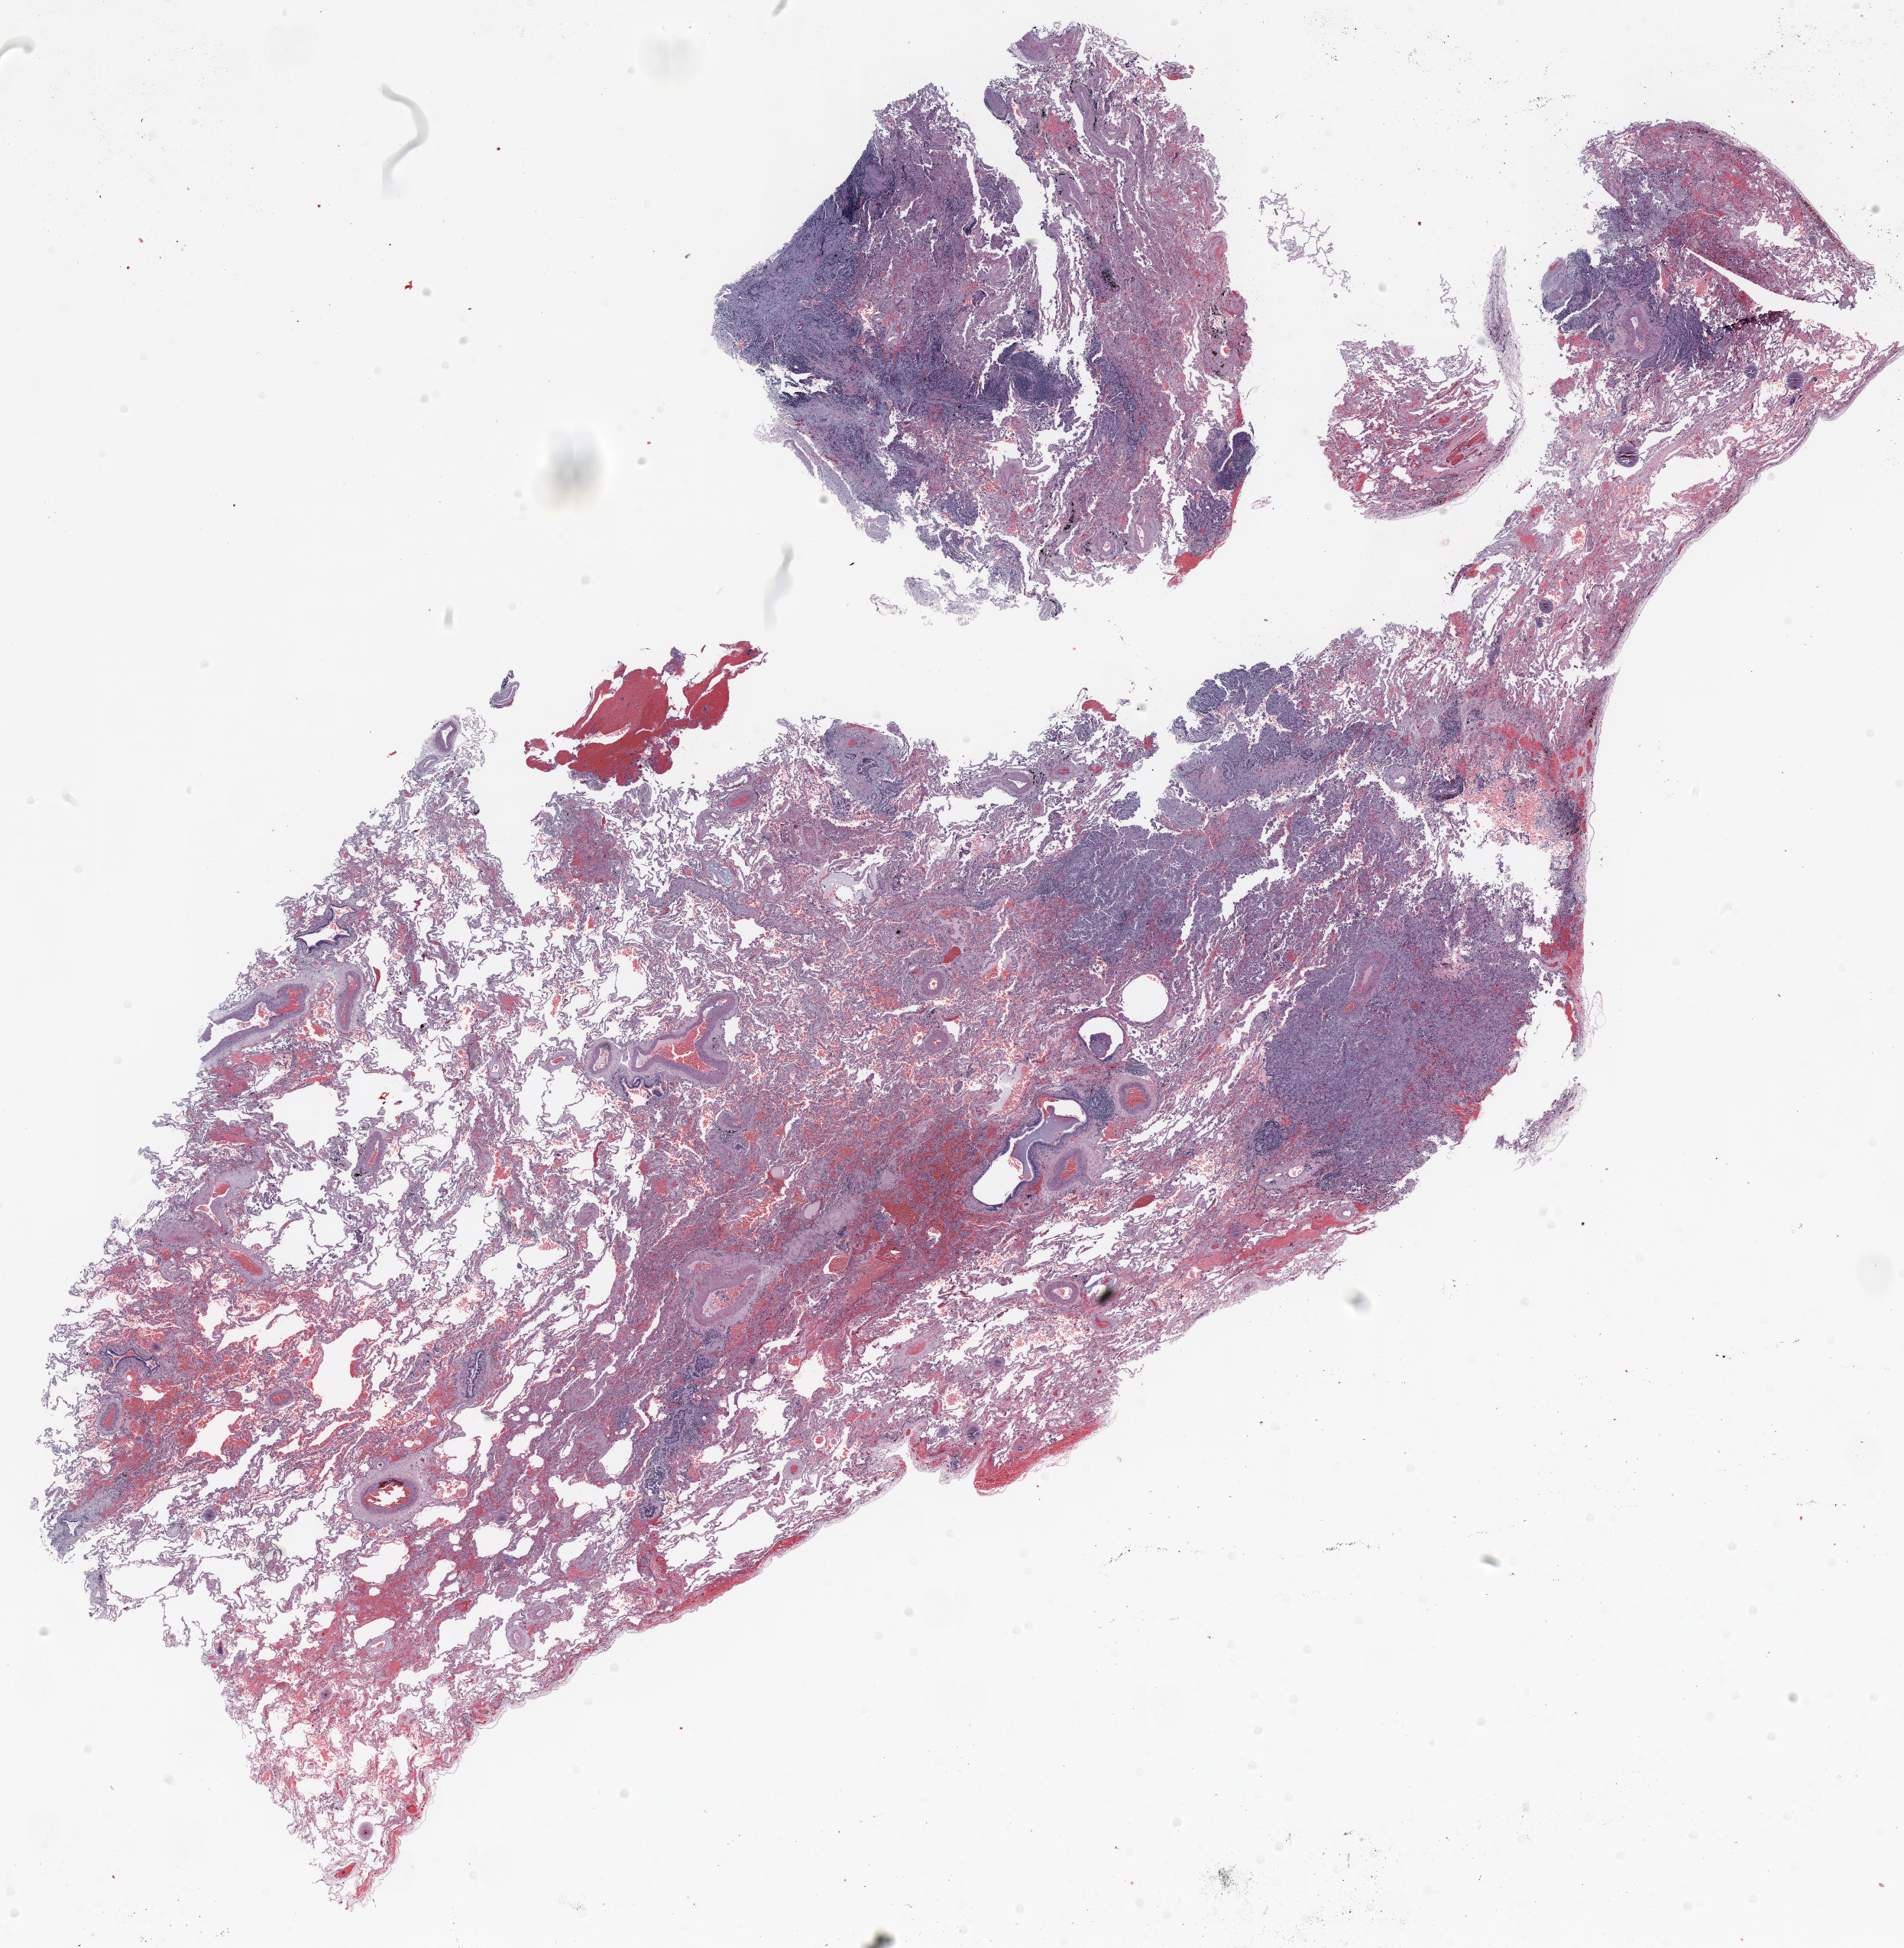
Whole-slide histology image, Hematoxylin and eosin (H&E) stained — a low-resolution overview of the entire scanned area, about 20.0 x 20.5 mm; FFPE section; lung tissue. Female patient, aged 73 at enrolment. Current smoker at enrolment. Grade: moderately differentiated (G2).
Participant's lung-cancer diagnosis: Adenocarcinoma, NOS (ICD-O-3 8140/3). Tumour size (pathology): 12 mm. Stage (AJCC 6th edition): IIIB. Primary tumour location (clinical record): left upper lobe.